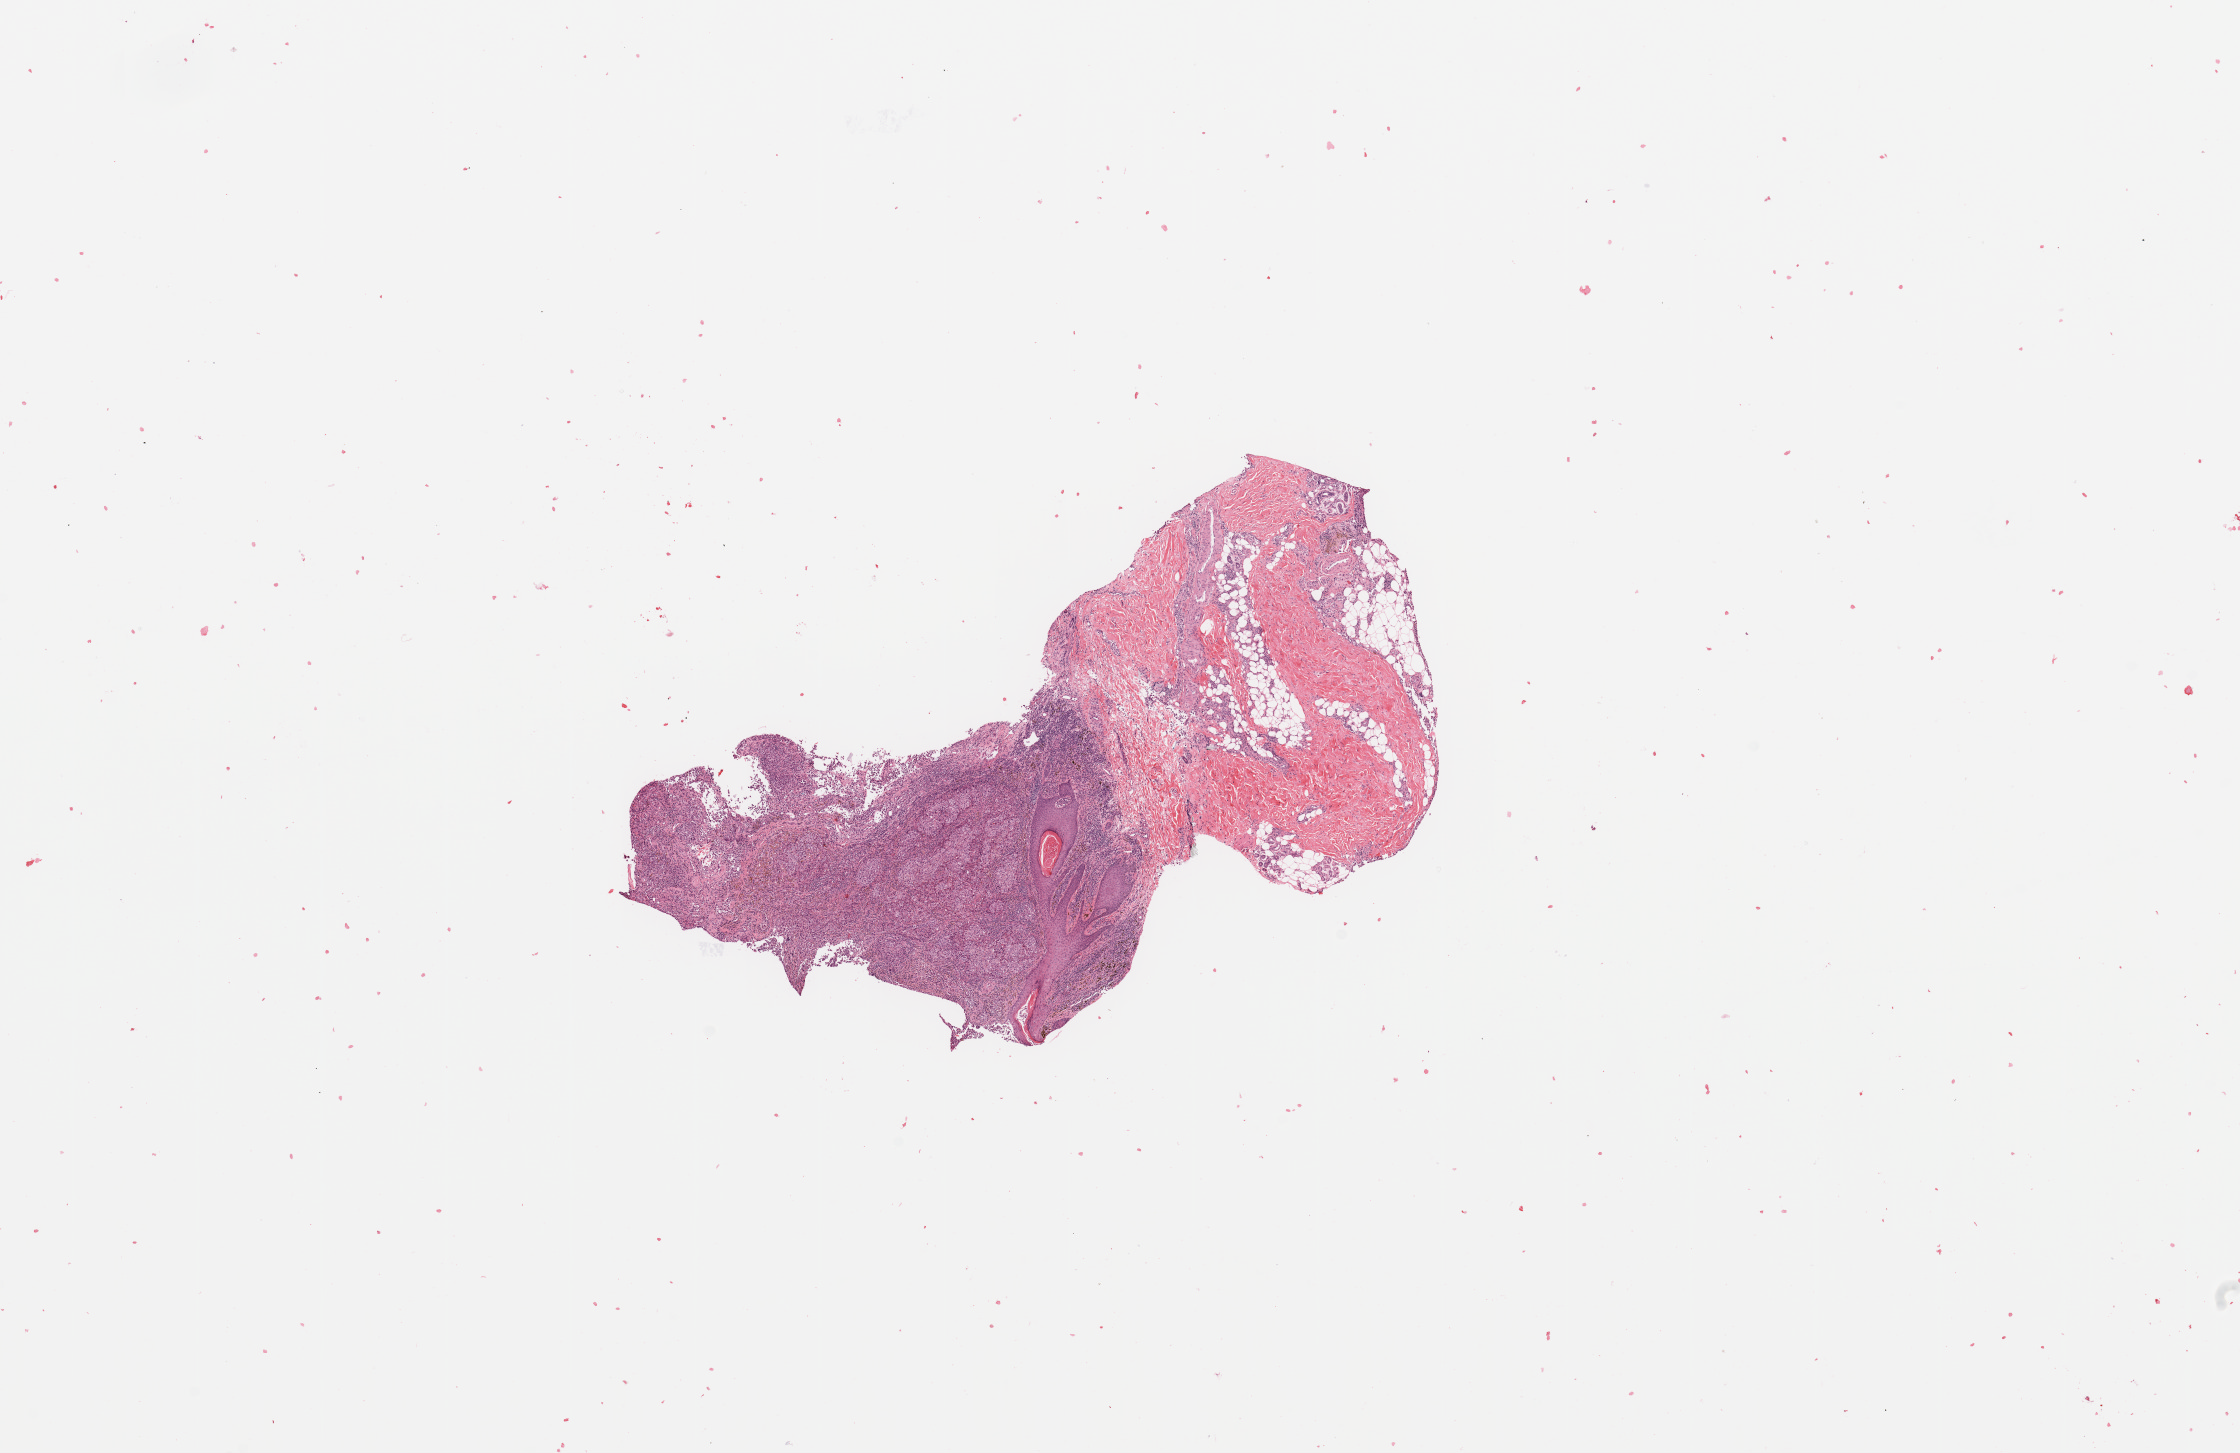
Hematoxylin and eosin (H&E) stained whole-slide image, a low-resolution overview of the entire scanned area, about 17.7 x 11.5 mm. Melanoma tumour tissue; sampled site not recorded. Female, 64 y/o.
• histologic diagnosis: Malignant melanoma, NOS
• AJCC pathologic stage: IIIC
• primary tumour site (as recorded): extremities